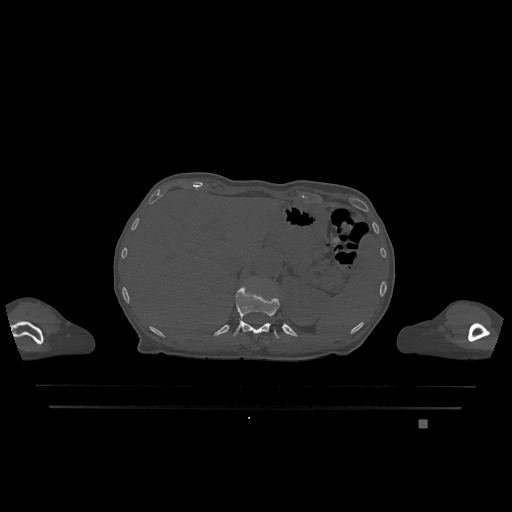
CT including the spine, one axial slice. Slice 529 of 1317 in the series (ordered by position). Bone window (W 1800 / L 400 HU). 0.5 mm slice thickness. 512 × 512 image matrix, field of view 500 × 500 mm. Patient: female, 74 years. Case-level facts recorded for this patient, not image findings: primary cancer: lung.
Structures marked on this image (semi-automatic segmentation, software-assisted and operator-edited):
- T12 vertebra: bounding box <233,286,280,339> (left, top, right, bottom; pixels)